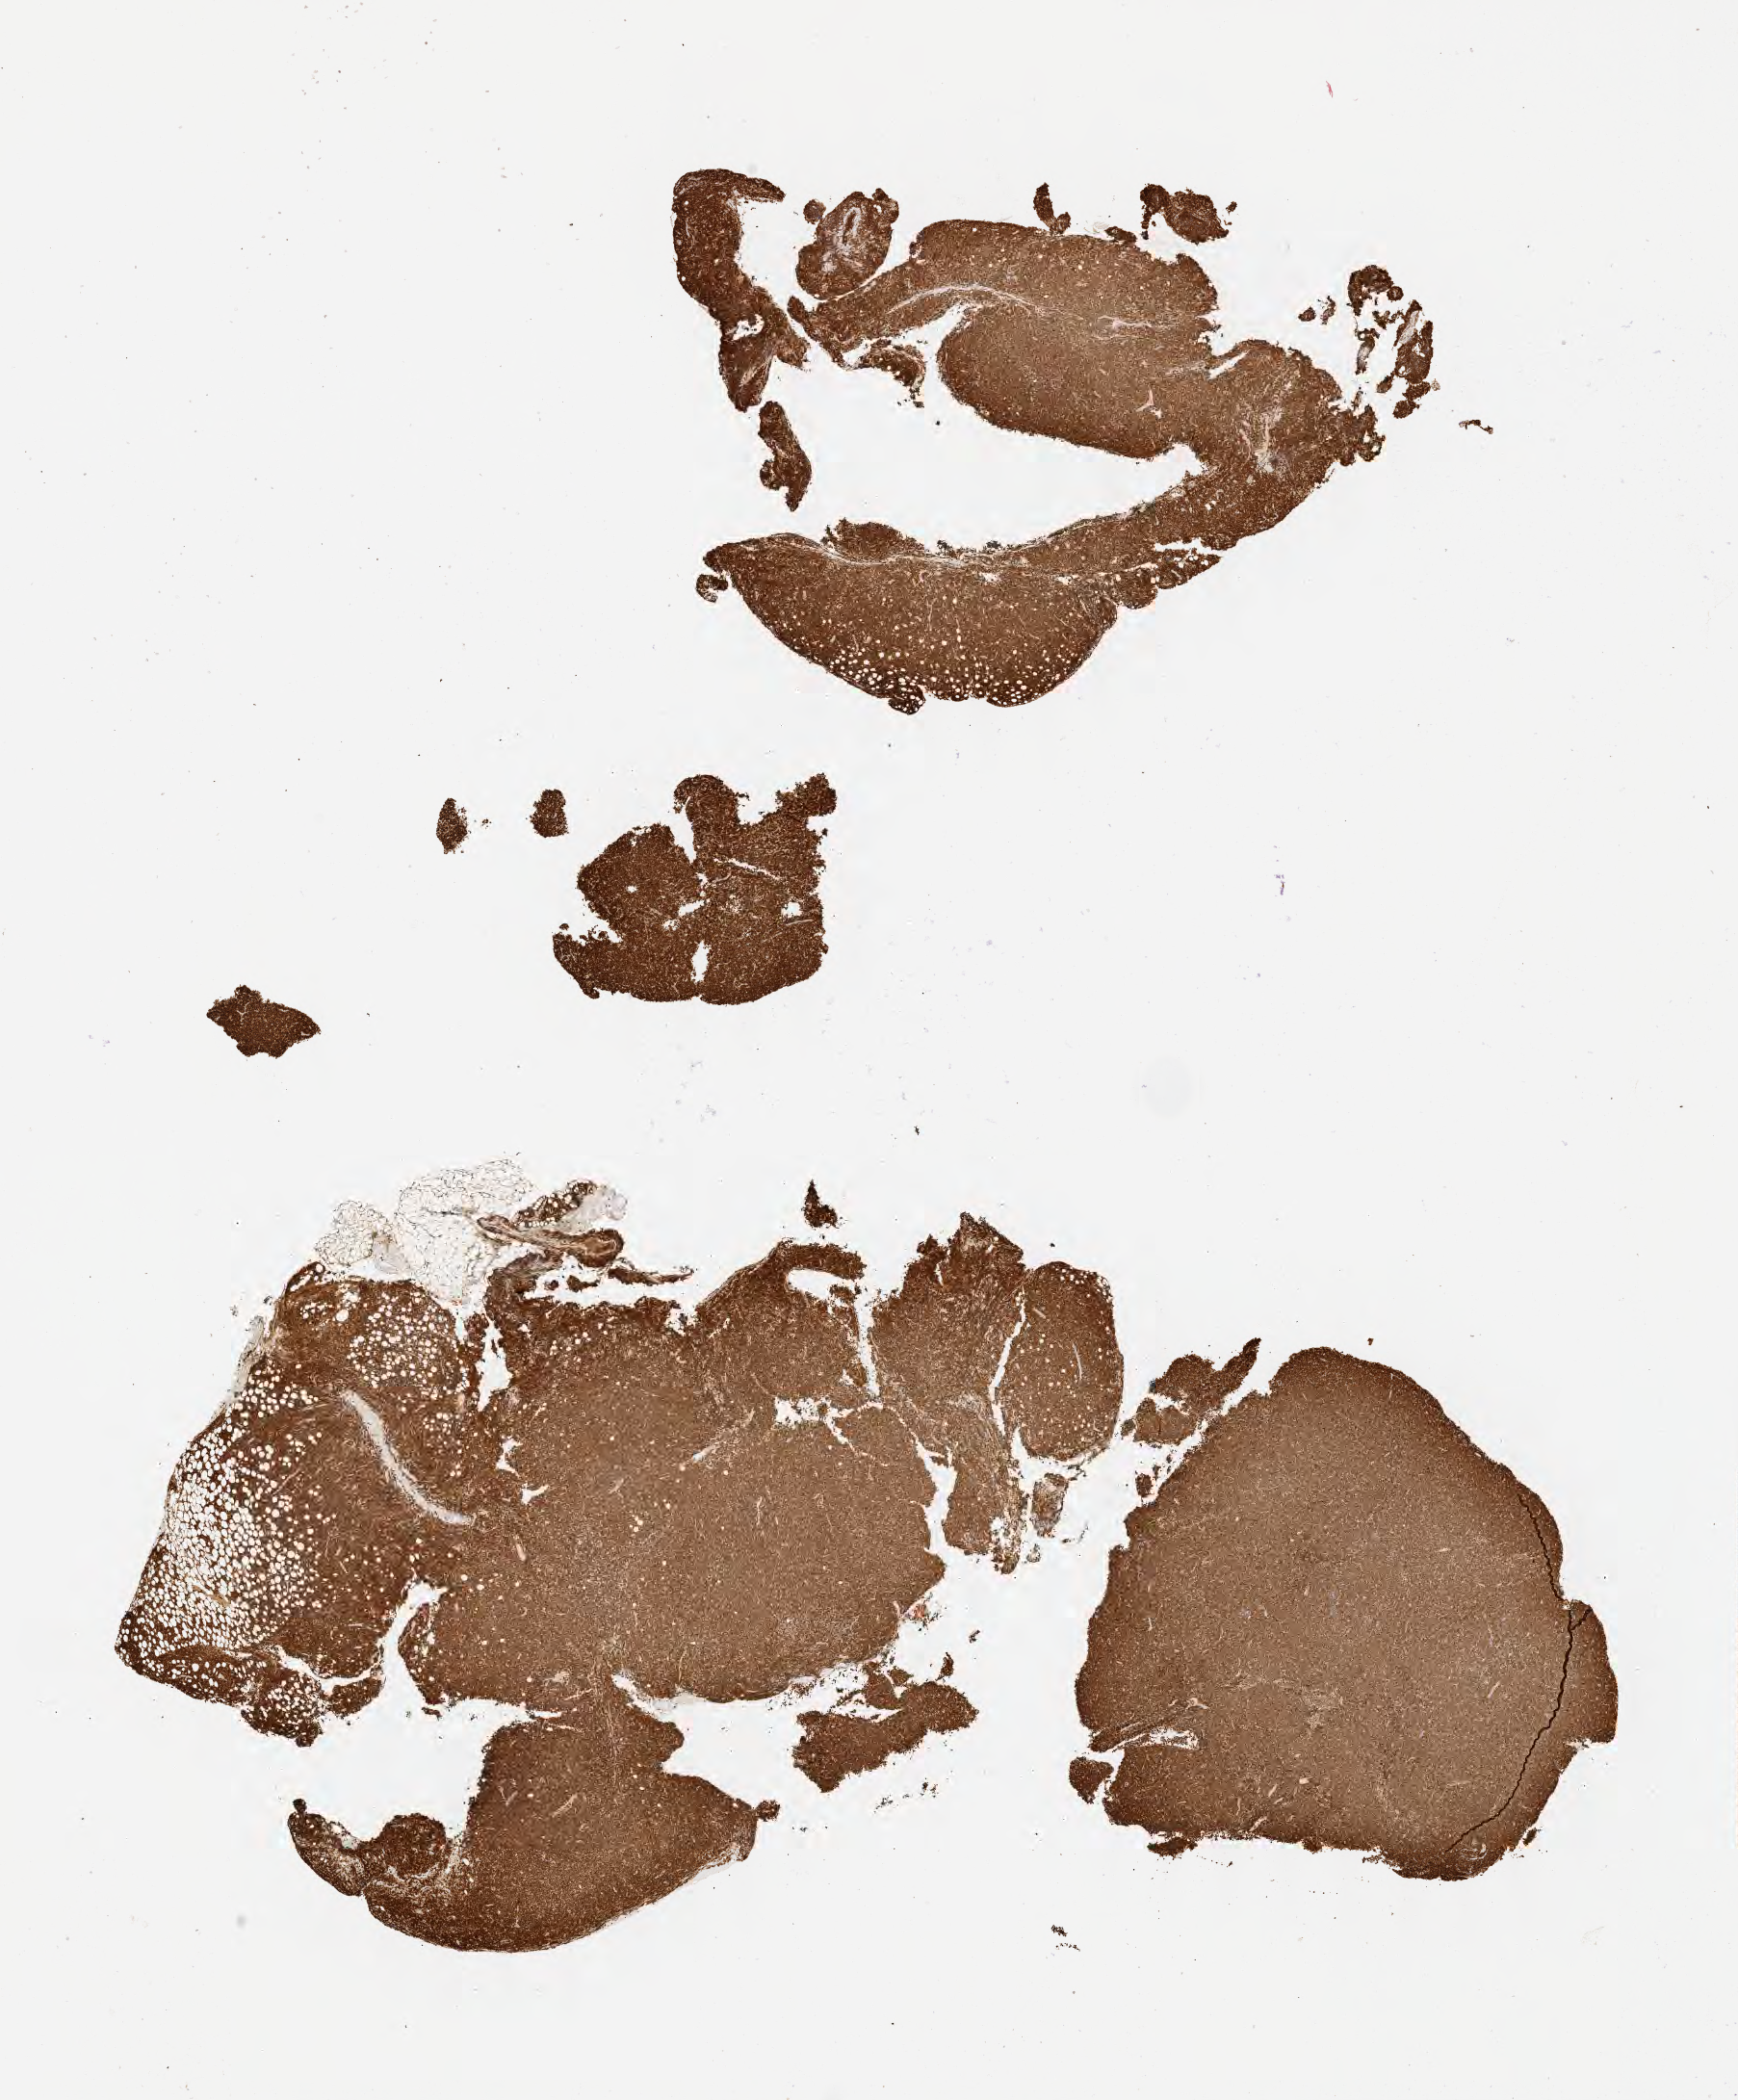
Whole-slide image, immunohistochemical stain for BCL2 — low-resolution overview of the scanned area, about 14.6 x 17.6 mm. Tumor tissue. Female patient, age 32 years.
Diagnosis: Diffuse large B-cell lymphoma, NOS.